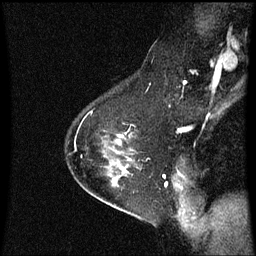
Breast MRI (dynamic contrast-enhanced), one sagittal slice. Dynamic contrast-enhanced series, image 2 of 3 at this slice position (ordered by acquisition). 1.5 T. TE 4.2 ms, TR 8.9 ms. 2 mm slice thickness. 256 × 256 image matrix, field of view 200 × 200 mm. Patient: female, 54 years. Case-level facts recorded for this patient, not image findings: setting: breast cancer imaged before/during neoadjuvant chemotherapy; receptor status: HER2-positive.
Structures marked on this image (semi-automatically segmented with operator editing):
- analysis volume of interest (the breast-tissue region the enhancement analysis was run in; not a lesion): bounding box (x1, y1, x2, y2) in pixels: (102, 132, 142, 169)
- tumour enhancement mask (voxels above the 70 % enhancement threshold inside the analysis volume of interest): (116, 136, 124, 145)